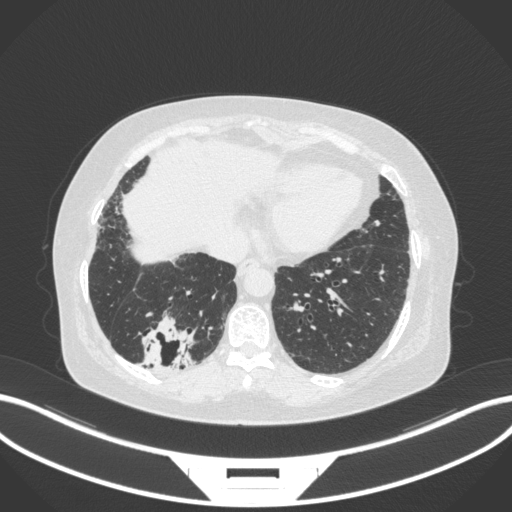
Chest CT, one axial slice; slice 53 of 303 in the series (ordered by position); reconstruction kernel B31f; 120 kVp; lung window (W 1500 / L -600 HU); 1 mm slice thickness; 512 × 512 image matrix. Patient: female, 65 years. Case-level facts recorded for this patient, not image findings: clinical TNM (as recorded): T2b N1 M0; histopathological grade: G1.
Annotated regions visible in this slice (bounding box drawn by a radiologist):
- lung tumour (recorded histology: adenocarcinoma): bounding box [x1, y1, x2, y2] px = [136, 313, 199, 375]